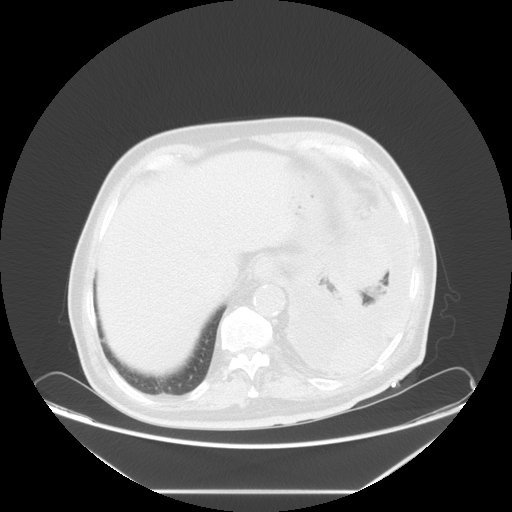
Chest CT, one axial slice. Position 14 of 63 along the scan axis. Reconstruction kernel STANDARD. 120 kVp. Lung window (W 1500 / L -600 HU). 5 mm slice thickness. 512 × 512 image matrix, field of view 448 × 448 mm. Male patient, age 67 years. From the clinical record (not read from this slice): clinical TNM (as recorded): T1b N1 M1a; histopathological grade: G3.
Structures marked on this image (rectangle marked by the reading radiologist):
- lung tumour (recorded histology: small cell carcinoma): box from (x=315, y=223) to (x=391, y=296) px